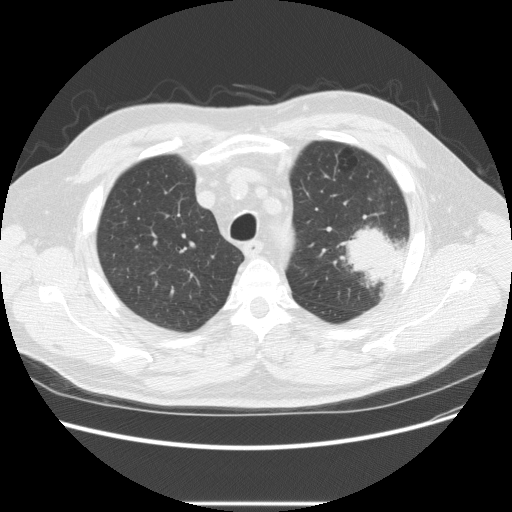
Axial slice from a low-dose chest CT screening exam; baseline screening round; lung window (W 1500 / L -600 HU); standard (soft-tissue) reconstruction kernel (STANDARD); slice 54 of 233 in the series; 512 × 512 image matrix. Male participant, aged 73 years at enrolment. Former smoker at enrolment.
Lesion marked by an expert reader, bounding box (x1, y1, x2, y2) in pixels: (332, 215, 413, 284). The screening reader recorded 2 non-calcified nodules or masses ≥4 mm on this exam (left upper lobe, right upper lobe); which of them this box marks is not recorded. Lung cancer was diagnosed 11 days after this screen: bronchiolo-alveolar adenocarcinoma, NOS, other location, well differentiated (G1), stage IV (AJCC 6th edition).